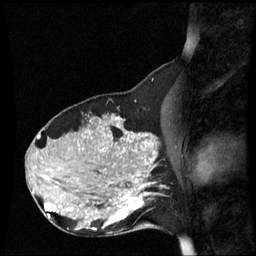
Breast MRI (dynamic contrast-enhanced), one sagittal slice. Position 25 of 60 along the scan axis. Dynamic contrast-enhanced series, image 2 of 3 at this slice position (ordered by acquisition). 1.5 T. TE 4.2 ms, TR 8.9 ms. 2.2 mm slice thickness. 256 × 256 image matrix, field of view 220 × 220 mm. Patient: female, 31 years. From the clinical record (not read from this slice): setting: breast cancer imaged before/during neoadjuvant chemotherapy; receptor status: HR-positive, HER2-negative.
Outlined on this slice (semi-automatic segmentation, software-assisted and operator-edited):
- analysis volume of interest (the breast-tissue region the enhancement analysis was run in; not a lesion): bounding box <90,180,152,237> (left, top, right, bottom; pixels)
- tumour enhancement mask (voxels above the 70 % enhancement threshold inside the analysis volume of interest): <93,180,151,231>